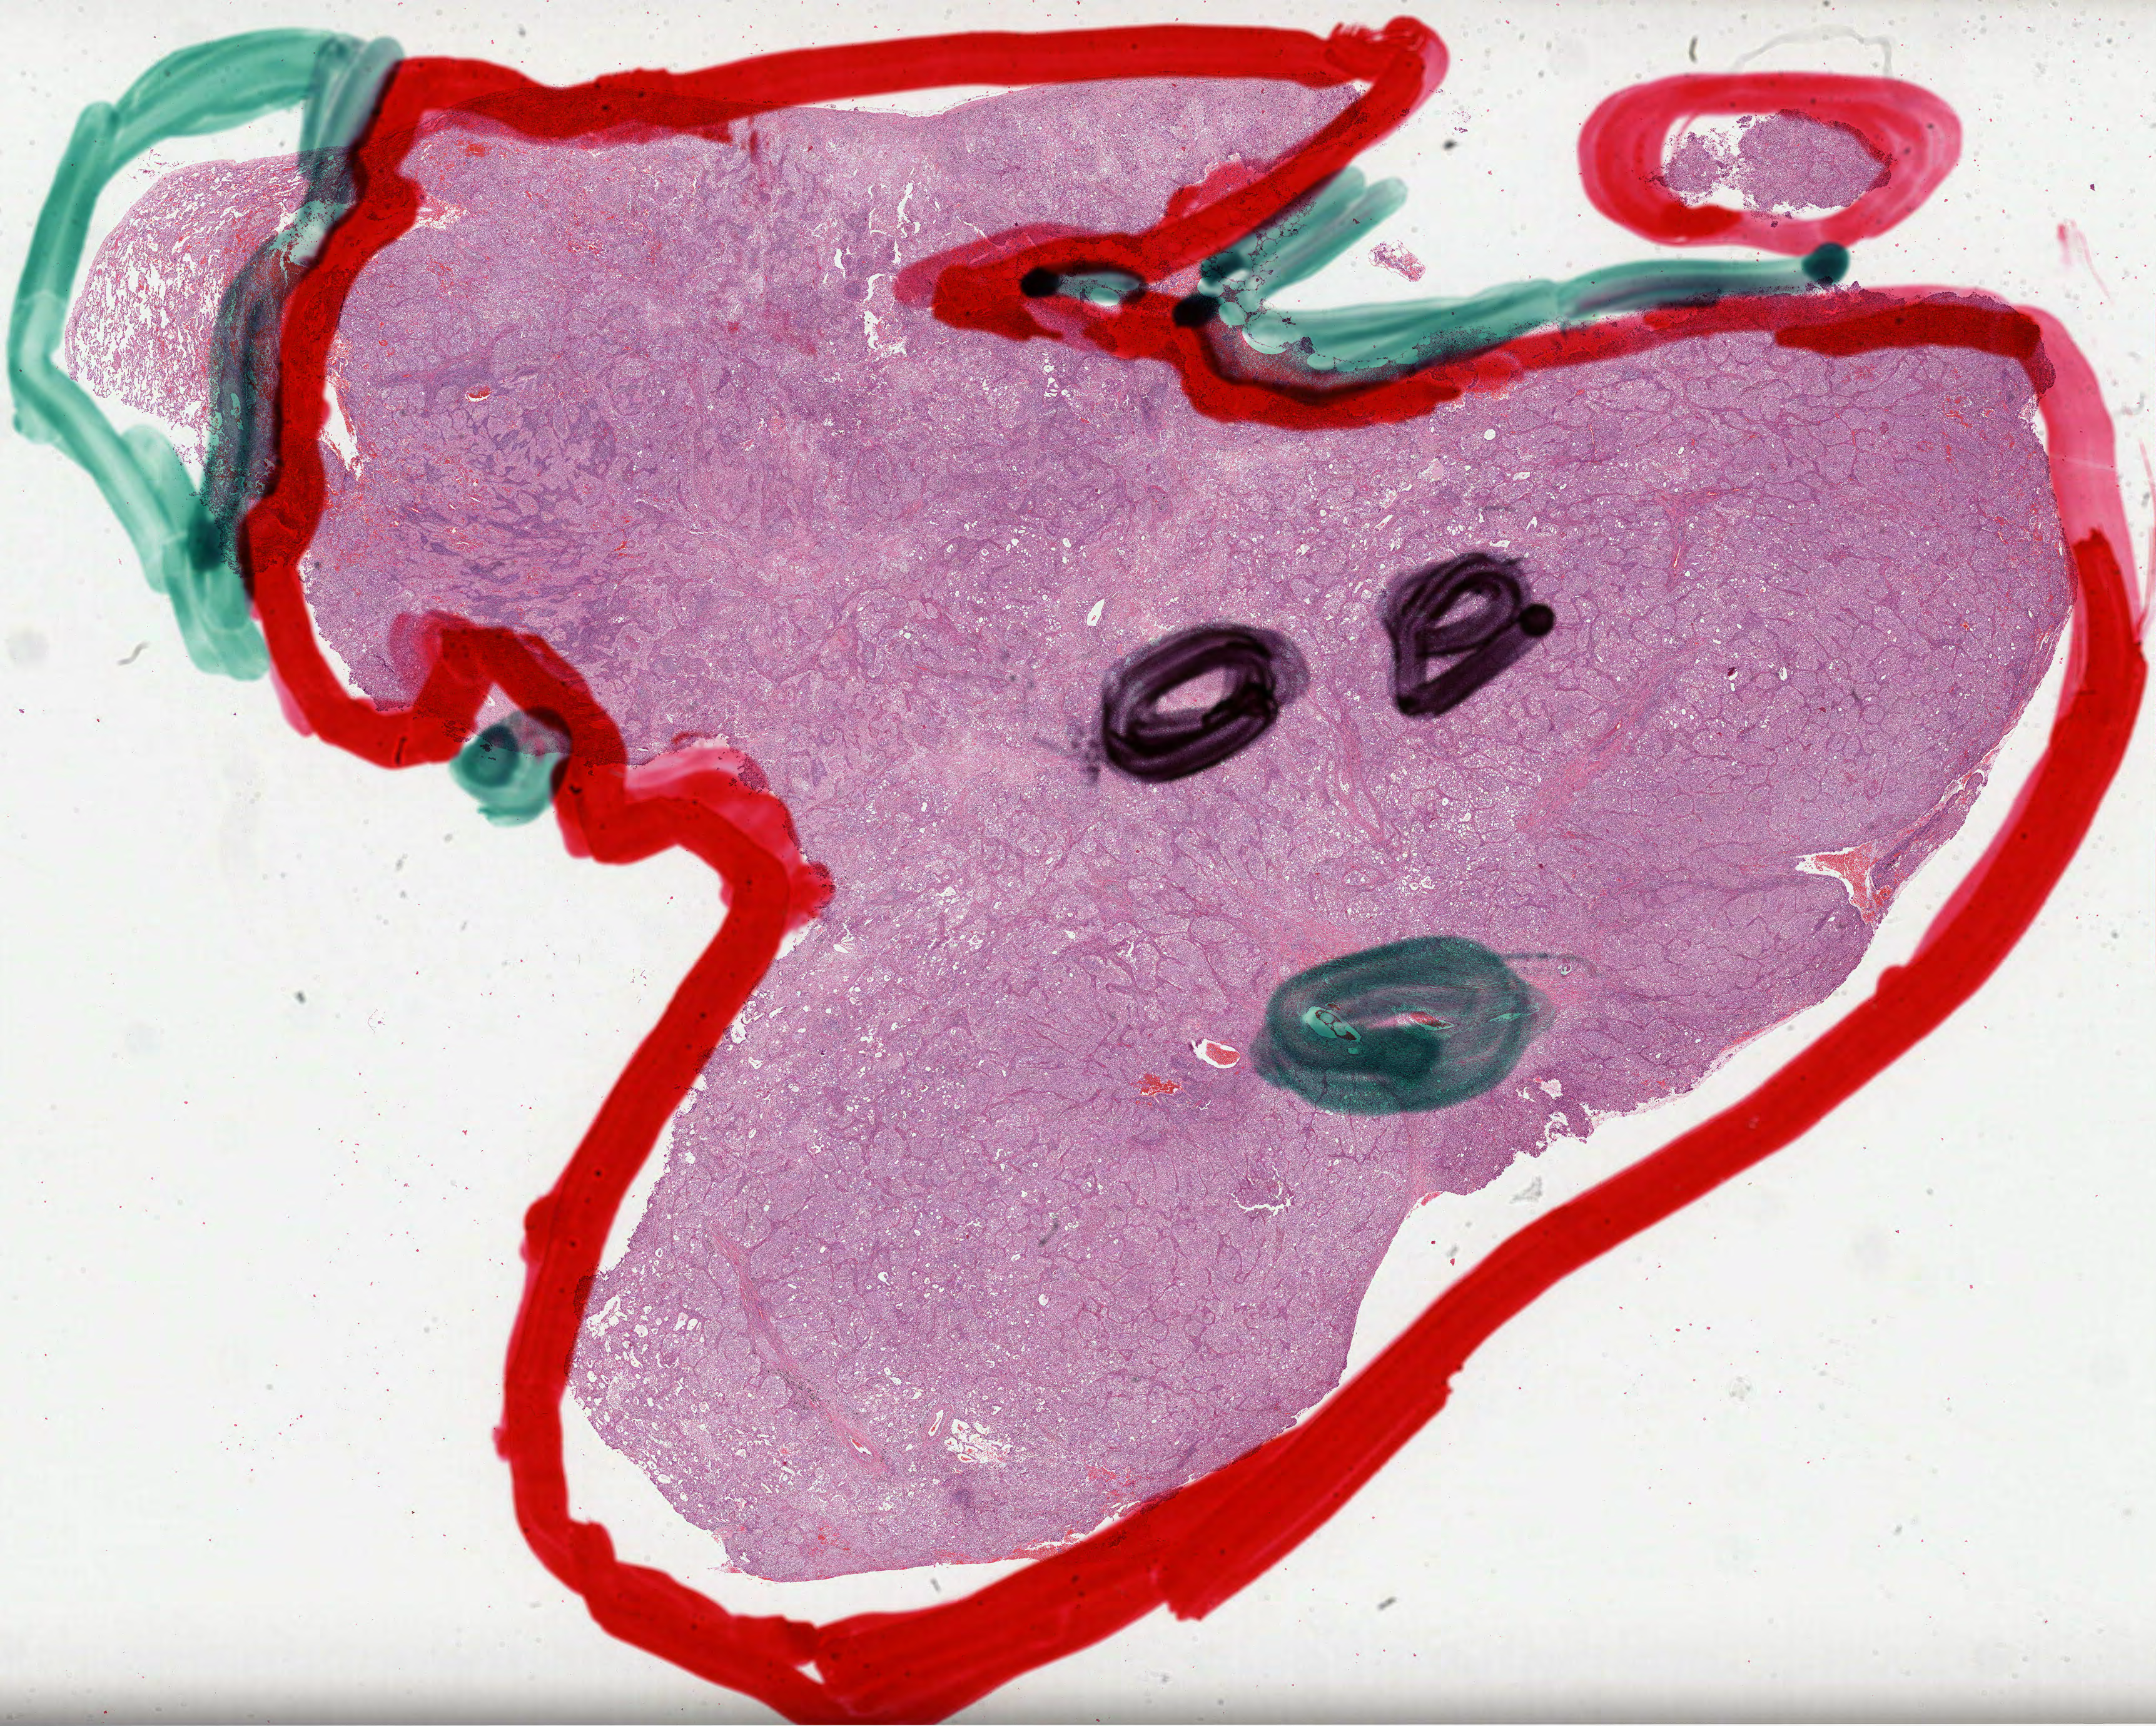
H&E whole-slide image, shown as a low-resolution overview of the whole scanned area (about 27.8 x 22.3 mm); FFPE section; lung, primary tumour sample. Patient: female, age at initial diagnosis 69 years.
Laterality: left. TNM: T1b N0 M0. Histologic diagnosis: Bronchiolo-alveolar adenocarcinoma, NOS (upper lobe, lung). AJCC pathologic stage: IA (7th edition).